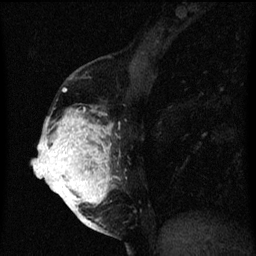
Breast MRI (dynamic contrast-enhanced), one sagittal slice; position 25 of 60 along the scan axis; dynamic contrast-enhanced series, image 2 of 3 at this slice position (ordered by acquisition); 1.5 T; TE 4.2 ms, TR 8 ms; 2 mm slice thickness; 256 × 256 image matrix, field of view 180 × 180 mm. Patient: female, 56 years.
Structures marked on this image (semi-automatically segmented with operator editing):
- analysis volume of interest (the breast-tissue region the enhancement analysis was run in; not a lesion): bounding box [x1, y1, x2, y2] px = [40, 108, 117, 219]
- tumour enhancement mask (voxels above the 70 % enhancement threshold inside the analysis volume of interest): [40, 112, 113, 219]